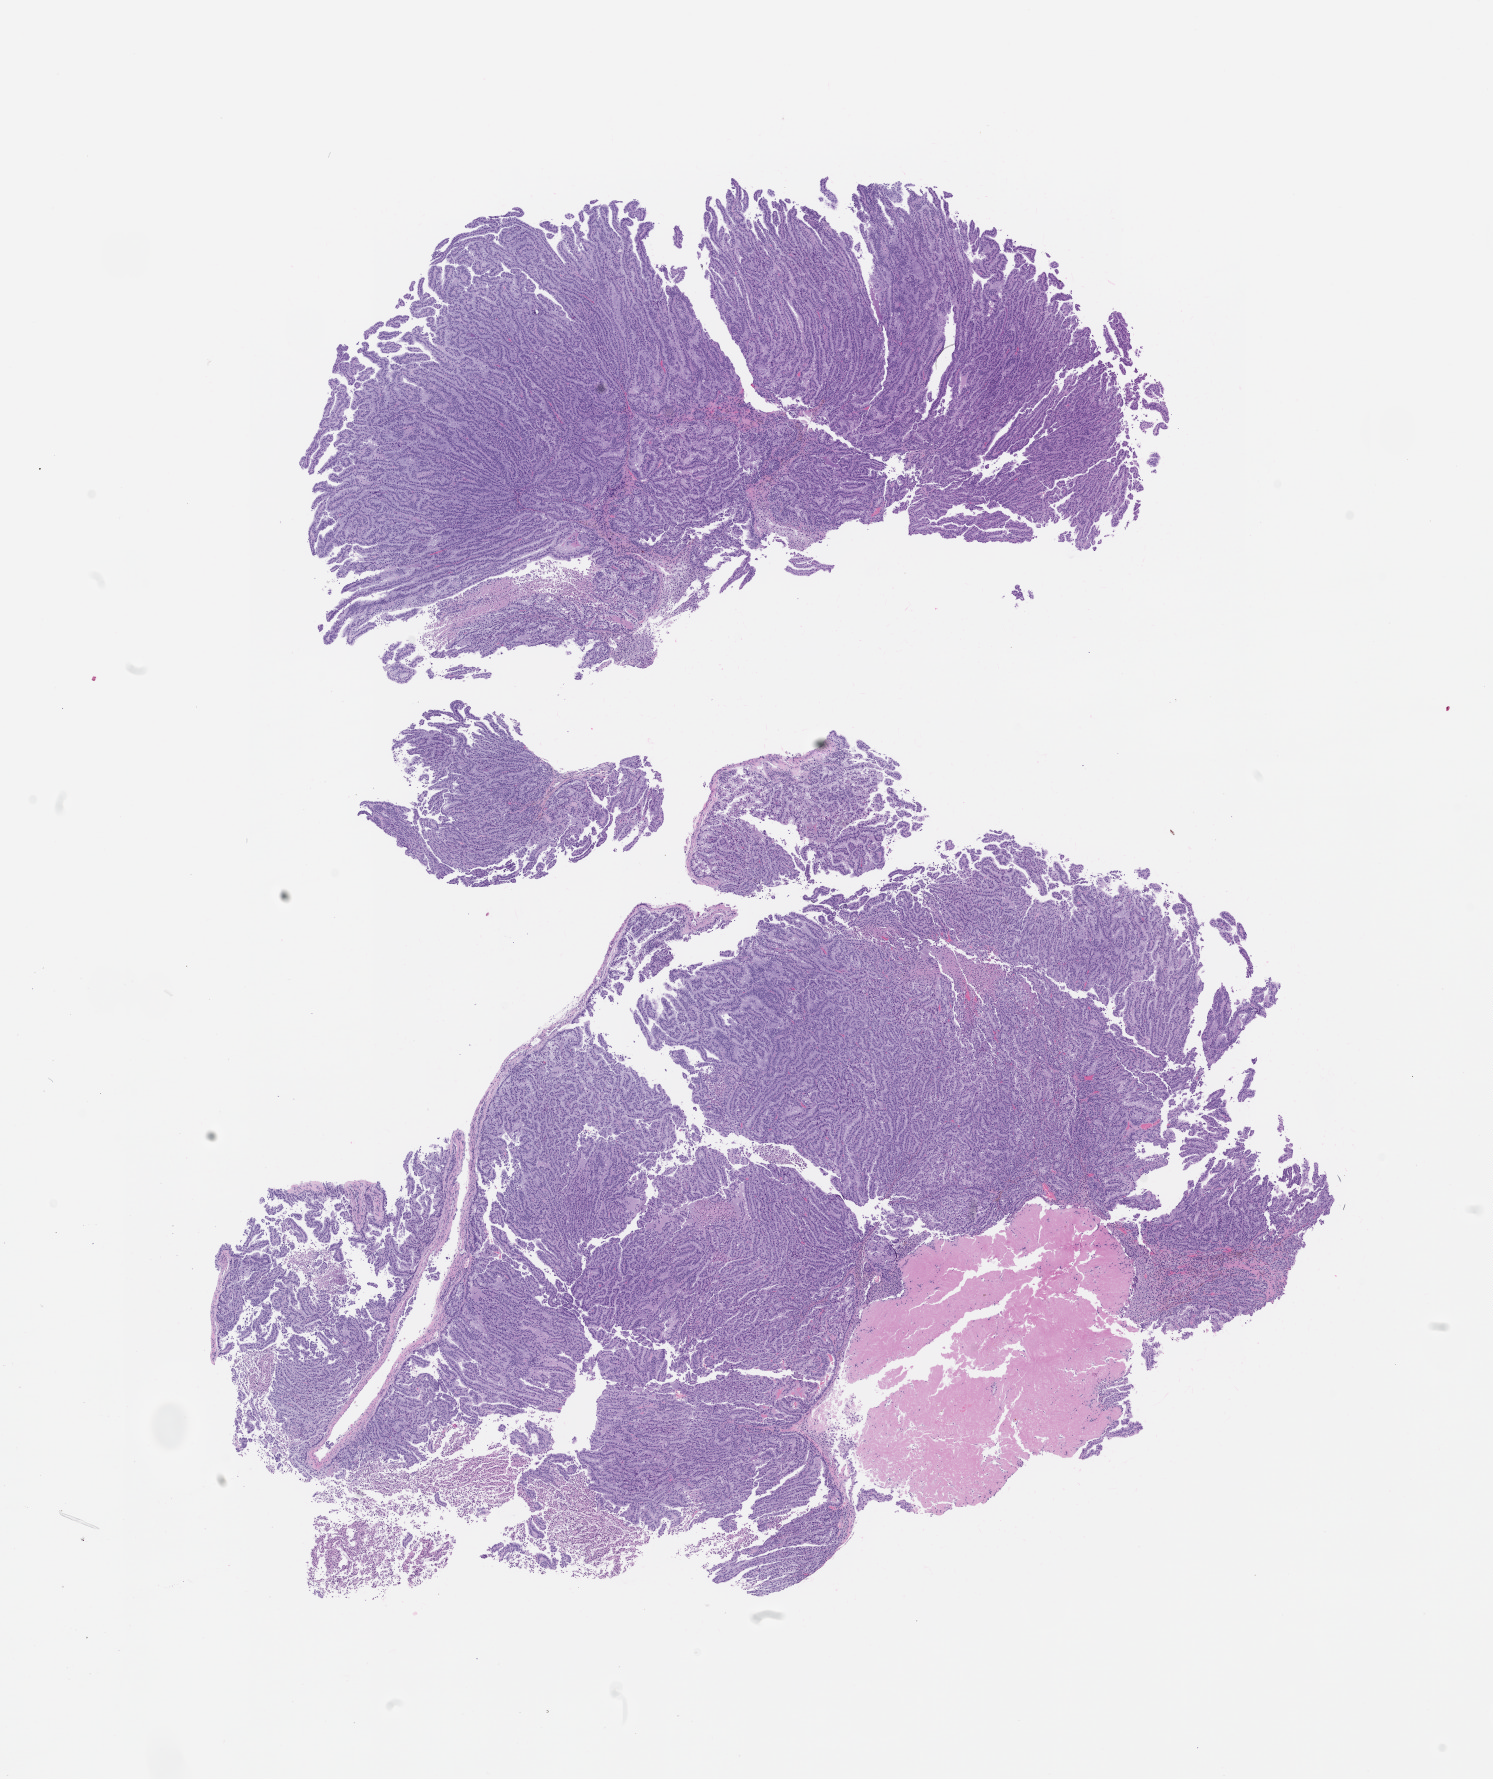
H&E whole-slide image of a patient-derived xenograft (PDX) tumor grown in a mouse, passage 1 — whole scanned area (about 12.0 x 14.3 mm) shown as a low-resolution overview. Formalin-fixed paraffin-embedded section. Originating tumor site category: genitourinary tract.
Originating patient diagnosis: Renal Cell Carcinoma, Not Otherwise Specified.